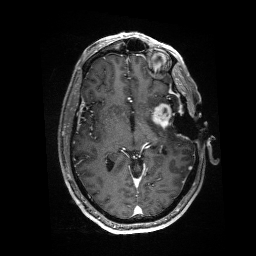
Brain MRI from a brain-tumour surgery series, one axial slice. Position 91 of 176 along the scan axis. T1-weighted post-contrast. 256 × 256 image matrix. Case-level facts recorded for this patient, not image findings: histopathology: Glioblastoma; WHO grade: 4; IDH mutation: no.
Outlined on this slice (outlined manually by an expert reader):
- residual tumour: box from (x=152, y=103) to (x=184, y=128) px